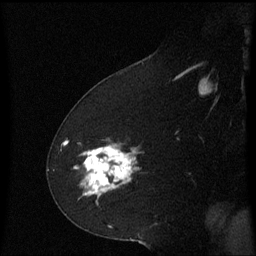
Breast MRI (dynamic contrast-enhanced), one sagittal slice. Slice 35 of 60 in the series (ordered by position). Dynamic contrast-enhanced series, image 2 of 3 at this slice position (ordered by acquisition). 1.5 T. TE 4.2 ms, TR 8.4 ms. 2.2 mm slice thickness. 256 × 256 image matrix. Patient: female, 60 years. From the clinical record (not read from this slice): setting: breast cancer imaged before/during neoadjuvant chemotherapy; receptor status: triple-negative.
Annotated regions visible in this slice (semi-automatic segmentation, software-assisted and operator-edited):
- analysis volume of interest (the breast-tissue region the enhancement analysis was run in; not a lesion): bounding box (x1, y1, x2, y2) in pixels: (75, 142, 141, 205)
- tumour enhancement mask (voxels above the 70 % enhancement threshold inside the analysis volume of interest): (84, 146, 137, 195)